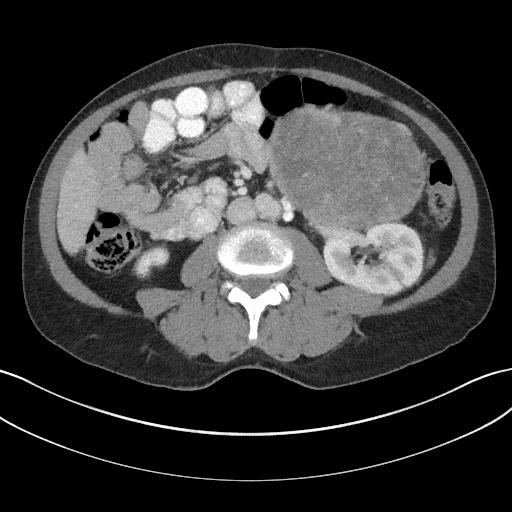
Contrast-enhanced abdominal CT, one axial slice. Slice 80 of 147 in the series (ordered by position). Reconstruction kernel I31f/3. 100 kVp. Soft-tissue window (W 400 / L 40 HU). 3 mm slice thickness. 512 × 512 image matrix, field of view 384 × 384 mm. Male patient, age 58 years. From the clinical record (not read from this slice): diagnosis: adrenocortical carcinoma; tumour side: left adrenal; tumour size at pathology: 22 cm; Ki-67 index: 26 %; stage (as recorded): 2.
Outlined on this slice (semi-automatic segmentation, software-assisted and operator-edited):
- mass: bounding box <272,108,425,225> (left, top, right, bottom; pixels)